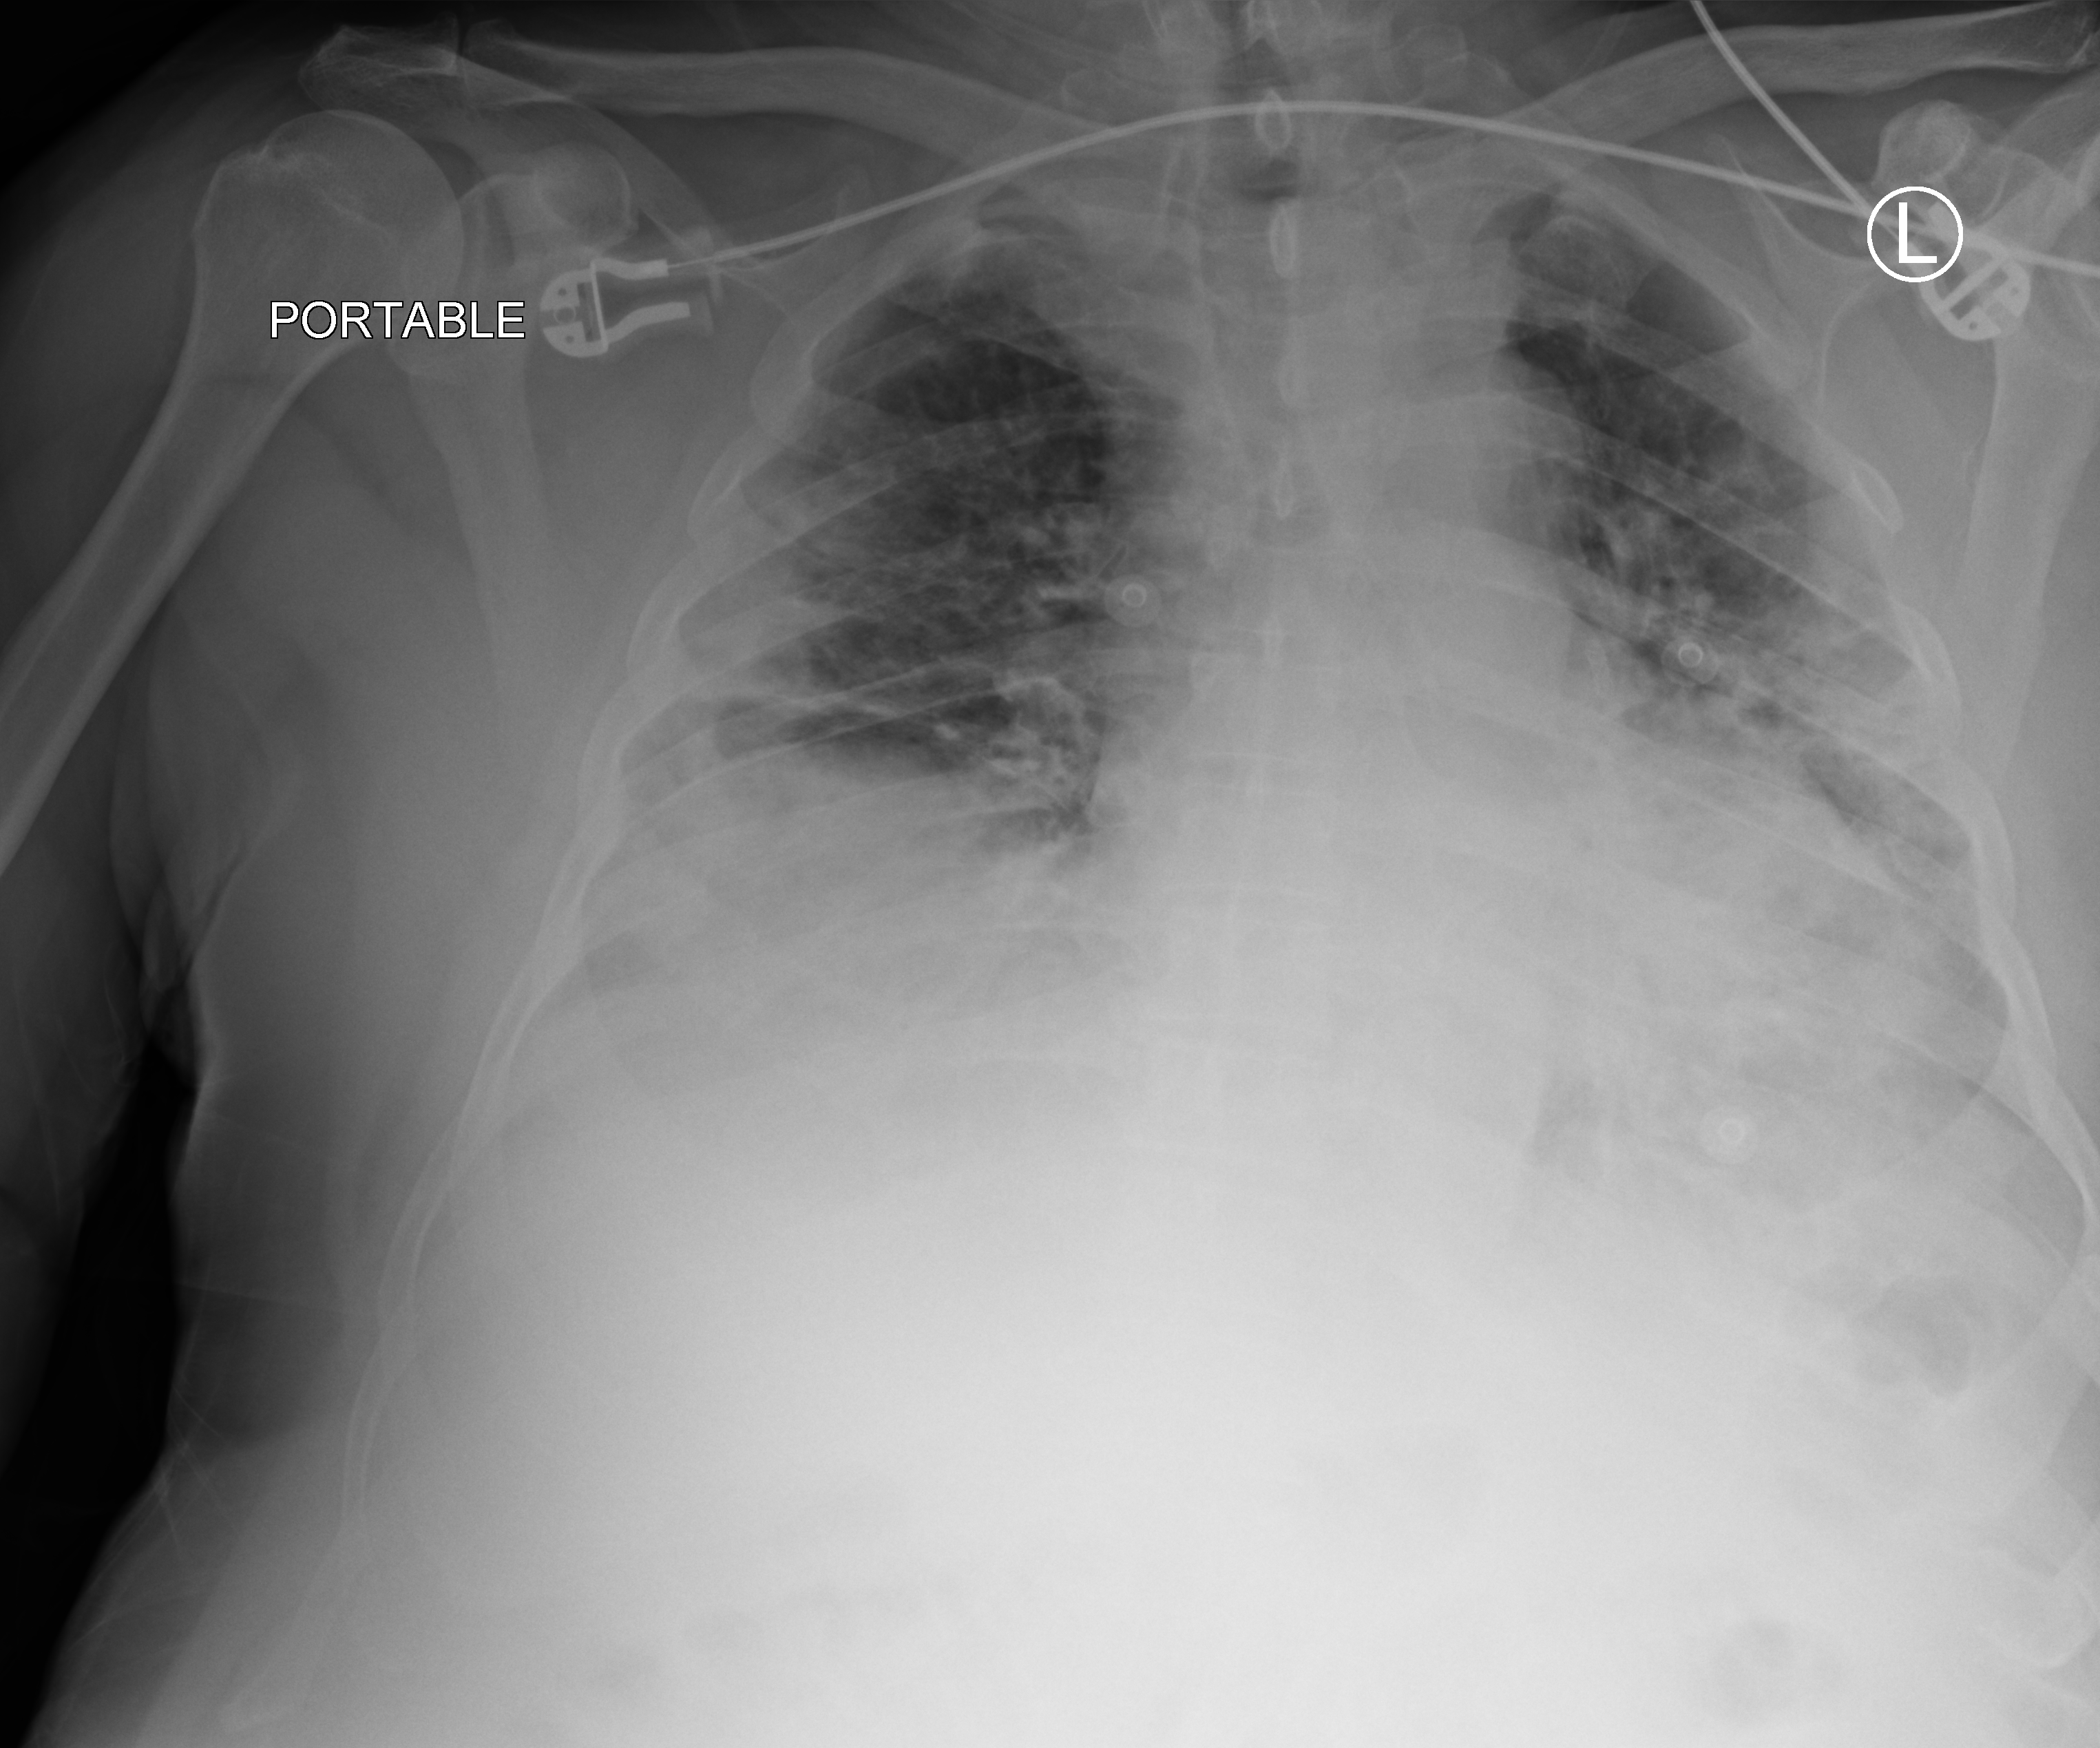
Bedside chest radiograph (computed radiography); anteroposterior (AP) projection. Male patient hospitalised with COVID-19, age 60–74 years.
Admission-level facts for this patient (not findings on this image; timing relative to this image not recorded):
- mechanically ventilated during this hospital stay: yes
- diabetes (admission record): yes
- admitted to intensive care during this hospital stay: yes